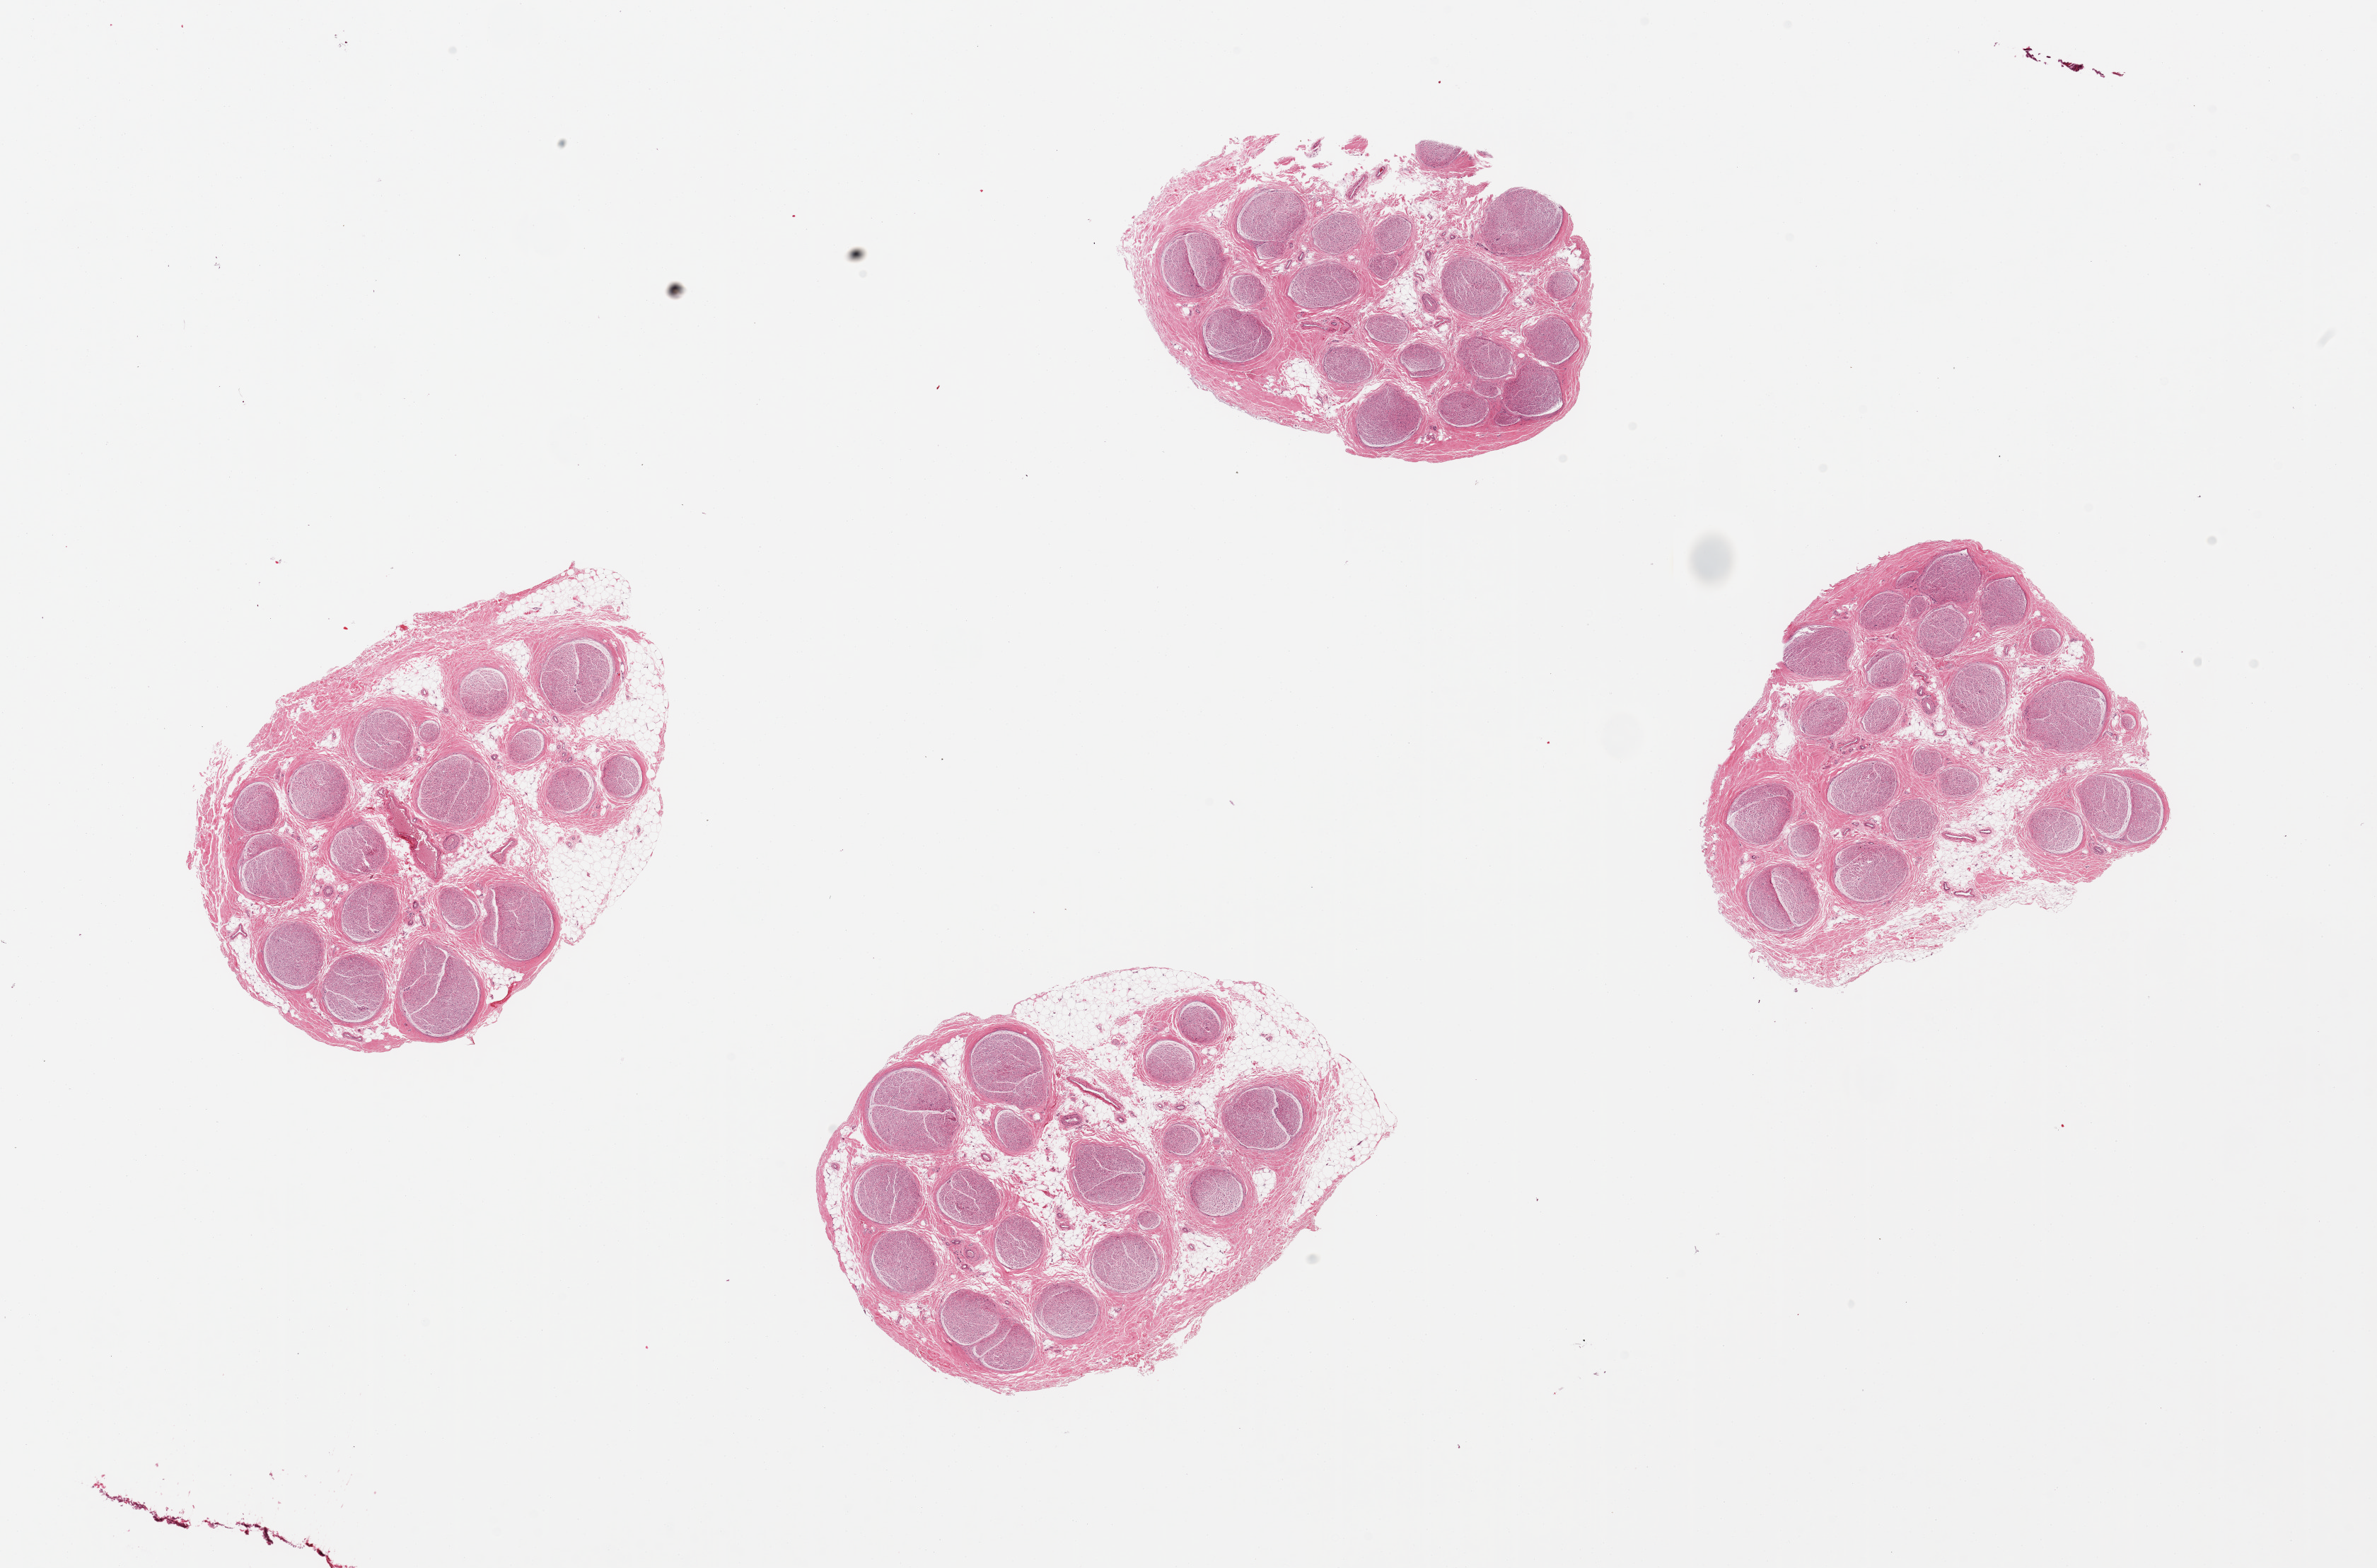
Whole-slide image, hematoxylin and eosin (H&E) stain, whole scanned area (about 26.6 x 17.5 mm, acquisition: 20x scan) shown as a low-resolution overview; PAXgene-fixed paraffin-embedded (PFPE) section; target tissue: tibial nerve; tissue donor sample. Donor: male.
Reviewer comment on this tissue sample: 4 pieces, generally clean sections.